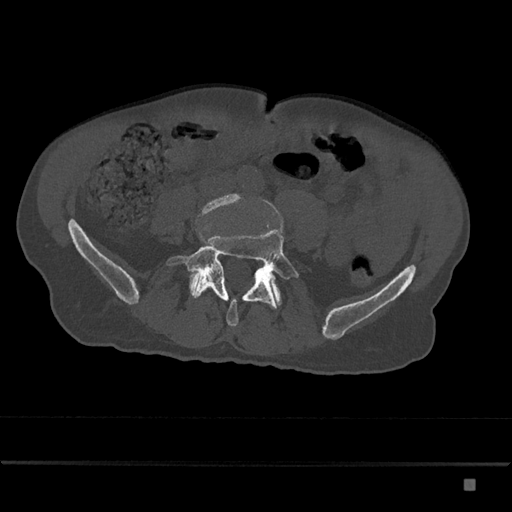
CT including the spine, one axial slice; slice 286 of 797 in the series (ordered by position); 120 kVp; bone window (W 1800 / L 400 HU); 0.5 mm slice thickness; 512 × 512 image matrix. Male patient, age 72 years. From the clinical record (not read from this slice): primary cancer: prostate.
Structures marked on this image (semi-automatic segmentation, software-assisted and operator-edited):
- L4 vertebra: box from (x=196, y=193) to (x=242, y=223) px
- L5 vertebra: (x=167, y=225)–(x=299, y=326)